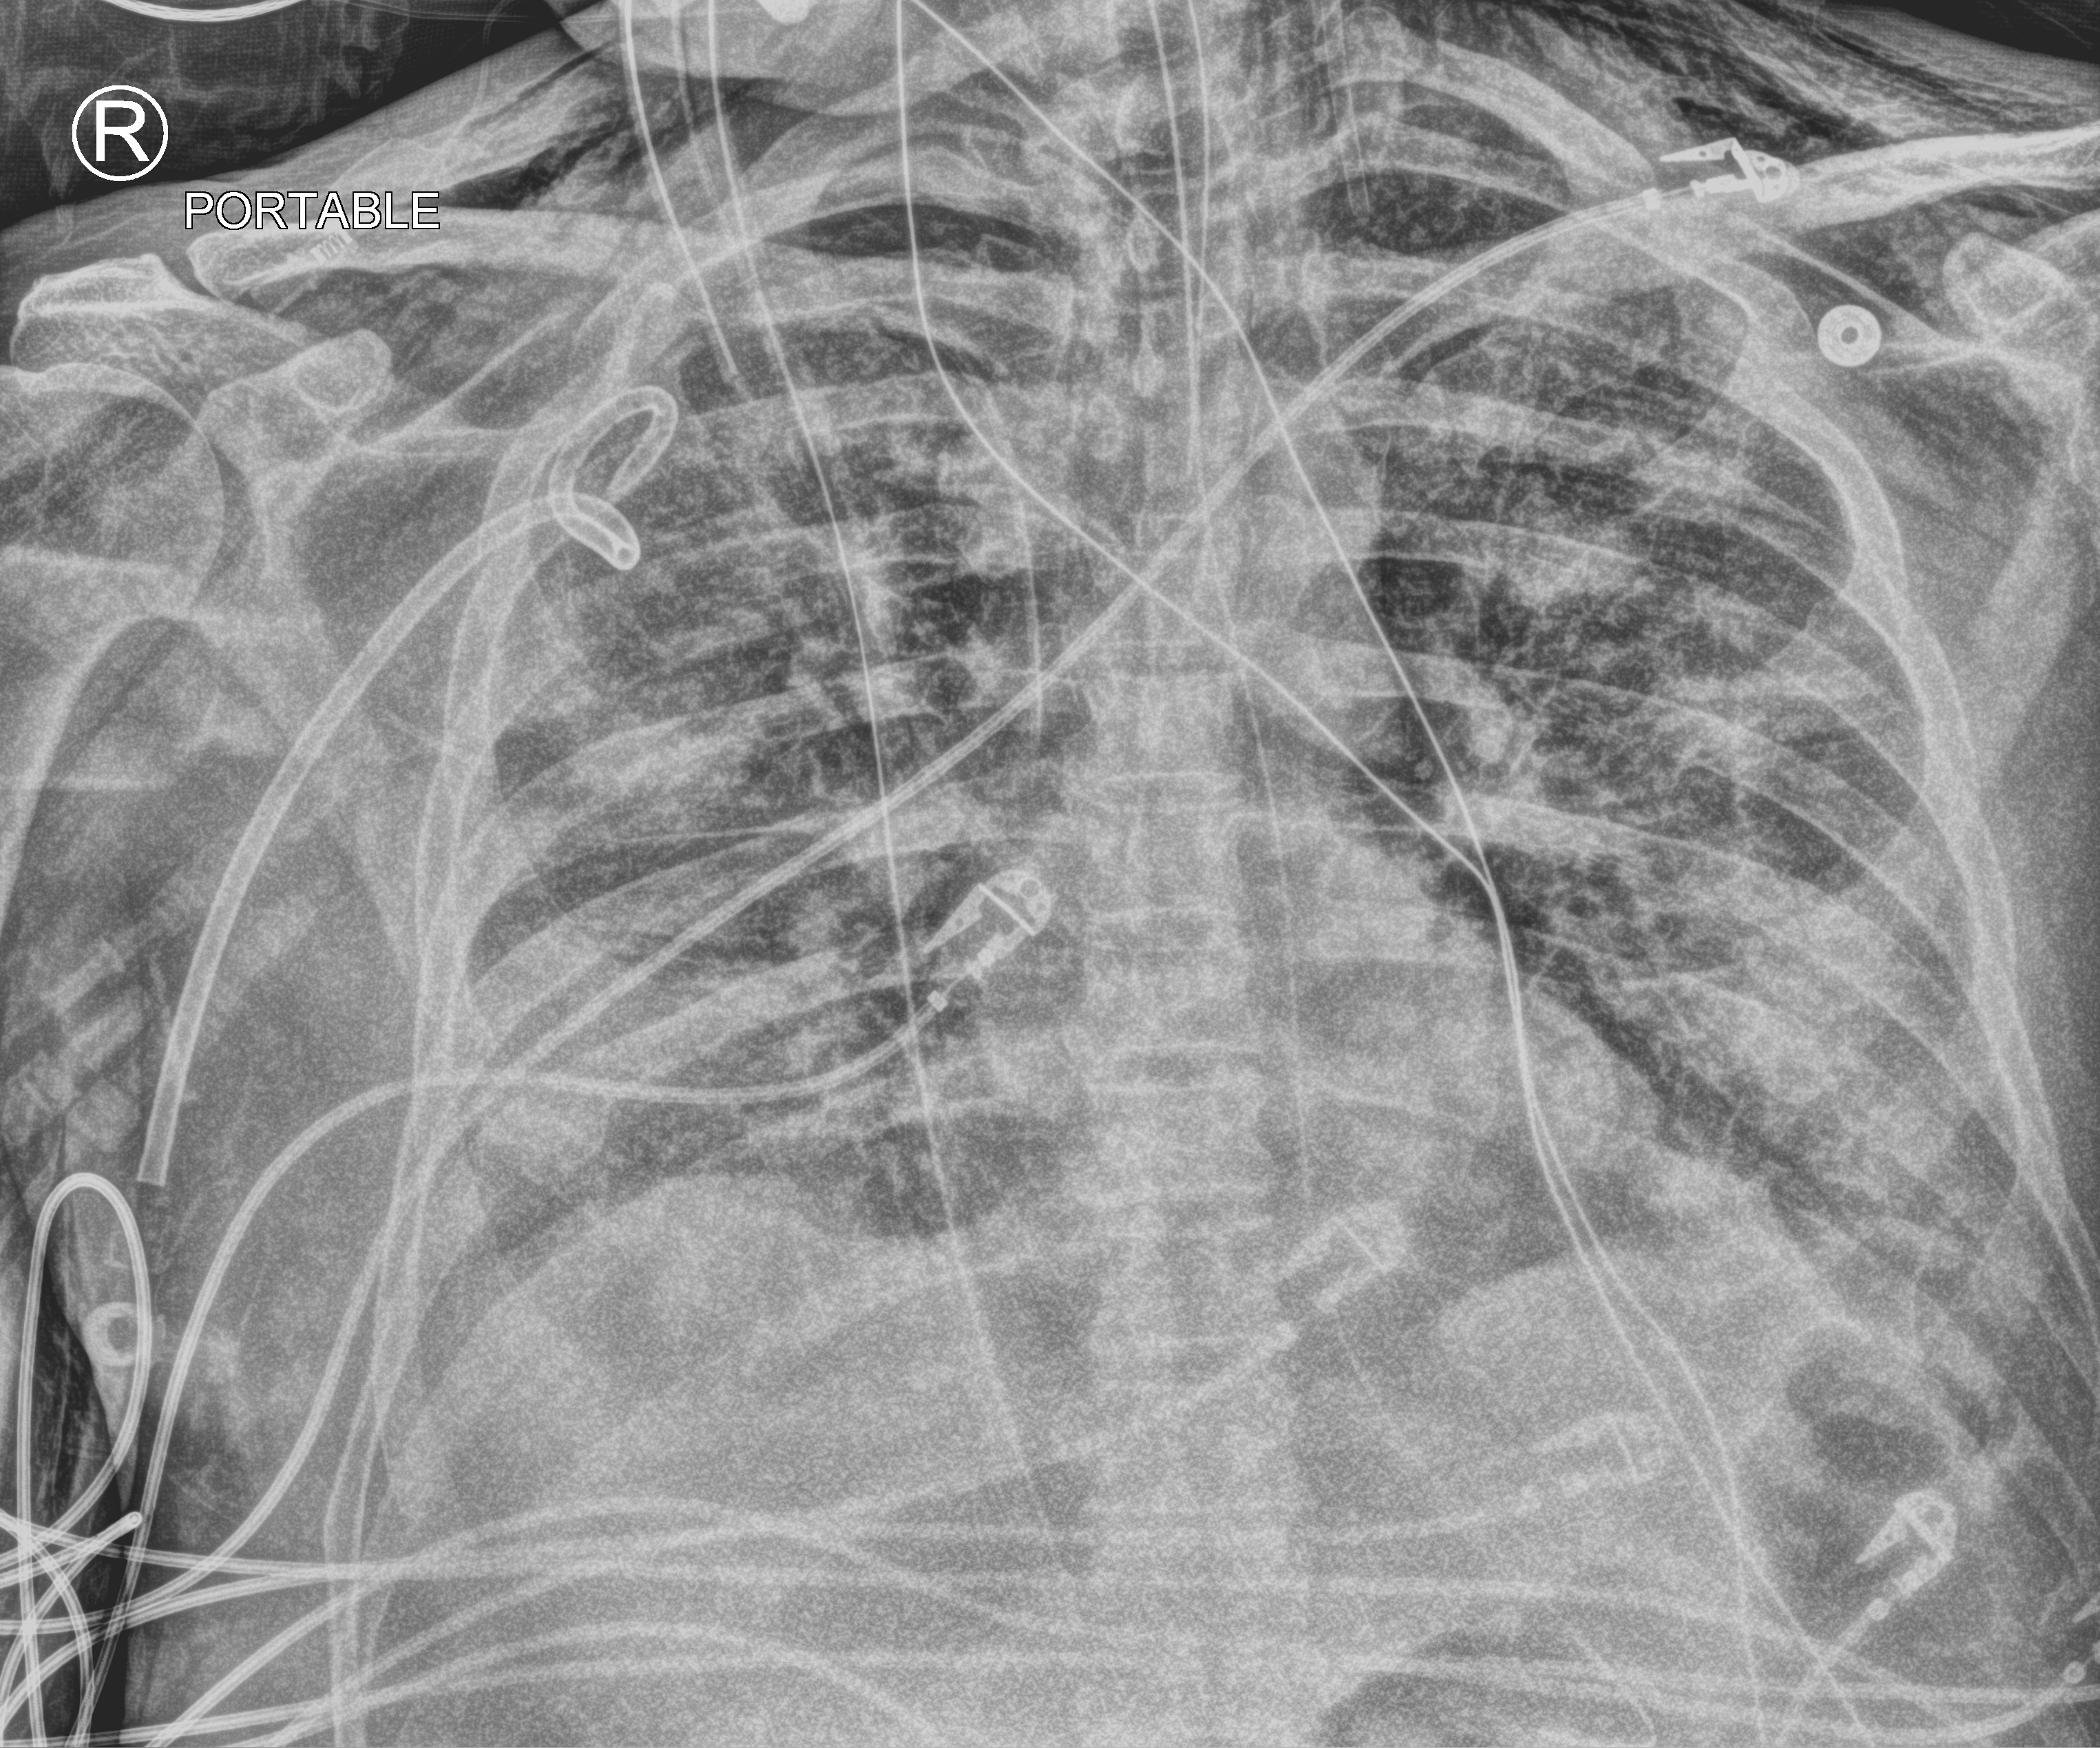
Portable chest radiograph, anteroposterior (AP) projection. Patient hospitalised with COVID-19; male, aged 60–74 years.
Admission-level facts for this patient (not findings on this image; timing relative to this image not recorded):
- length of hospital stay: 8 days
- smoking status (admission record): never
- other chronic lung disease (admission record): no